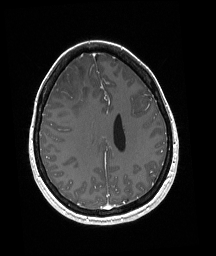
Brain MRI from a brain-tumour surgery series, one axial slice; position 73 of 192 along the scan axis; T1-weighted post-contrast; 1 mm slice thickness; 216 × 256 image matrix, field of view 211 × 250 mm. From the clinical record (not read from this slice): histopathology: Oligodendroglioma; WHO grade: 3; IDH mutation: yes.
Annotated regions visible in this slice (outlined manually by an expert reader):
- tumour: box from (x=69, y=85) to (x=86, y=91) px